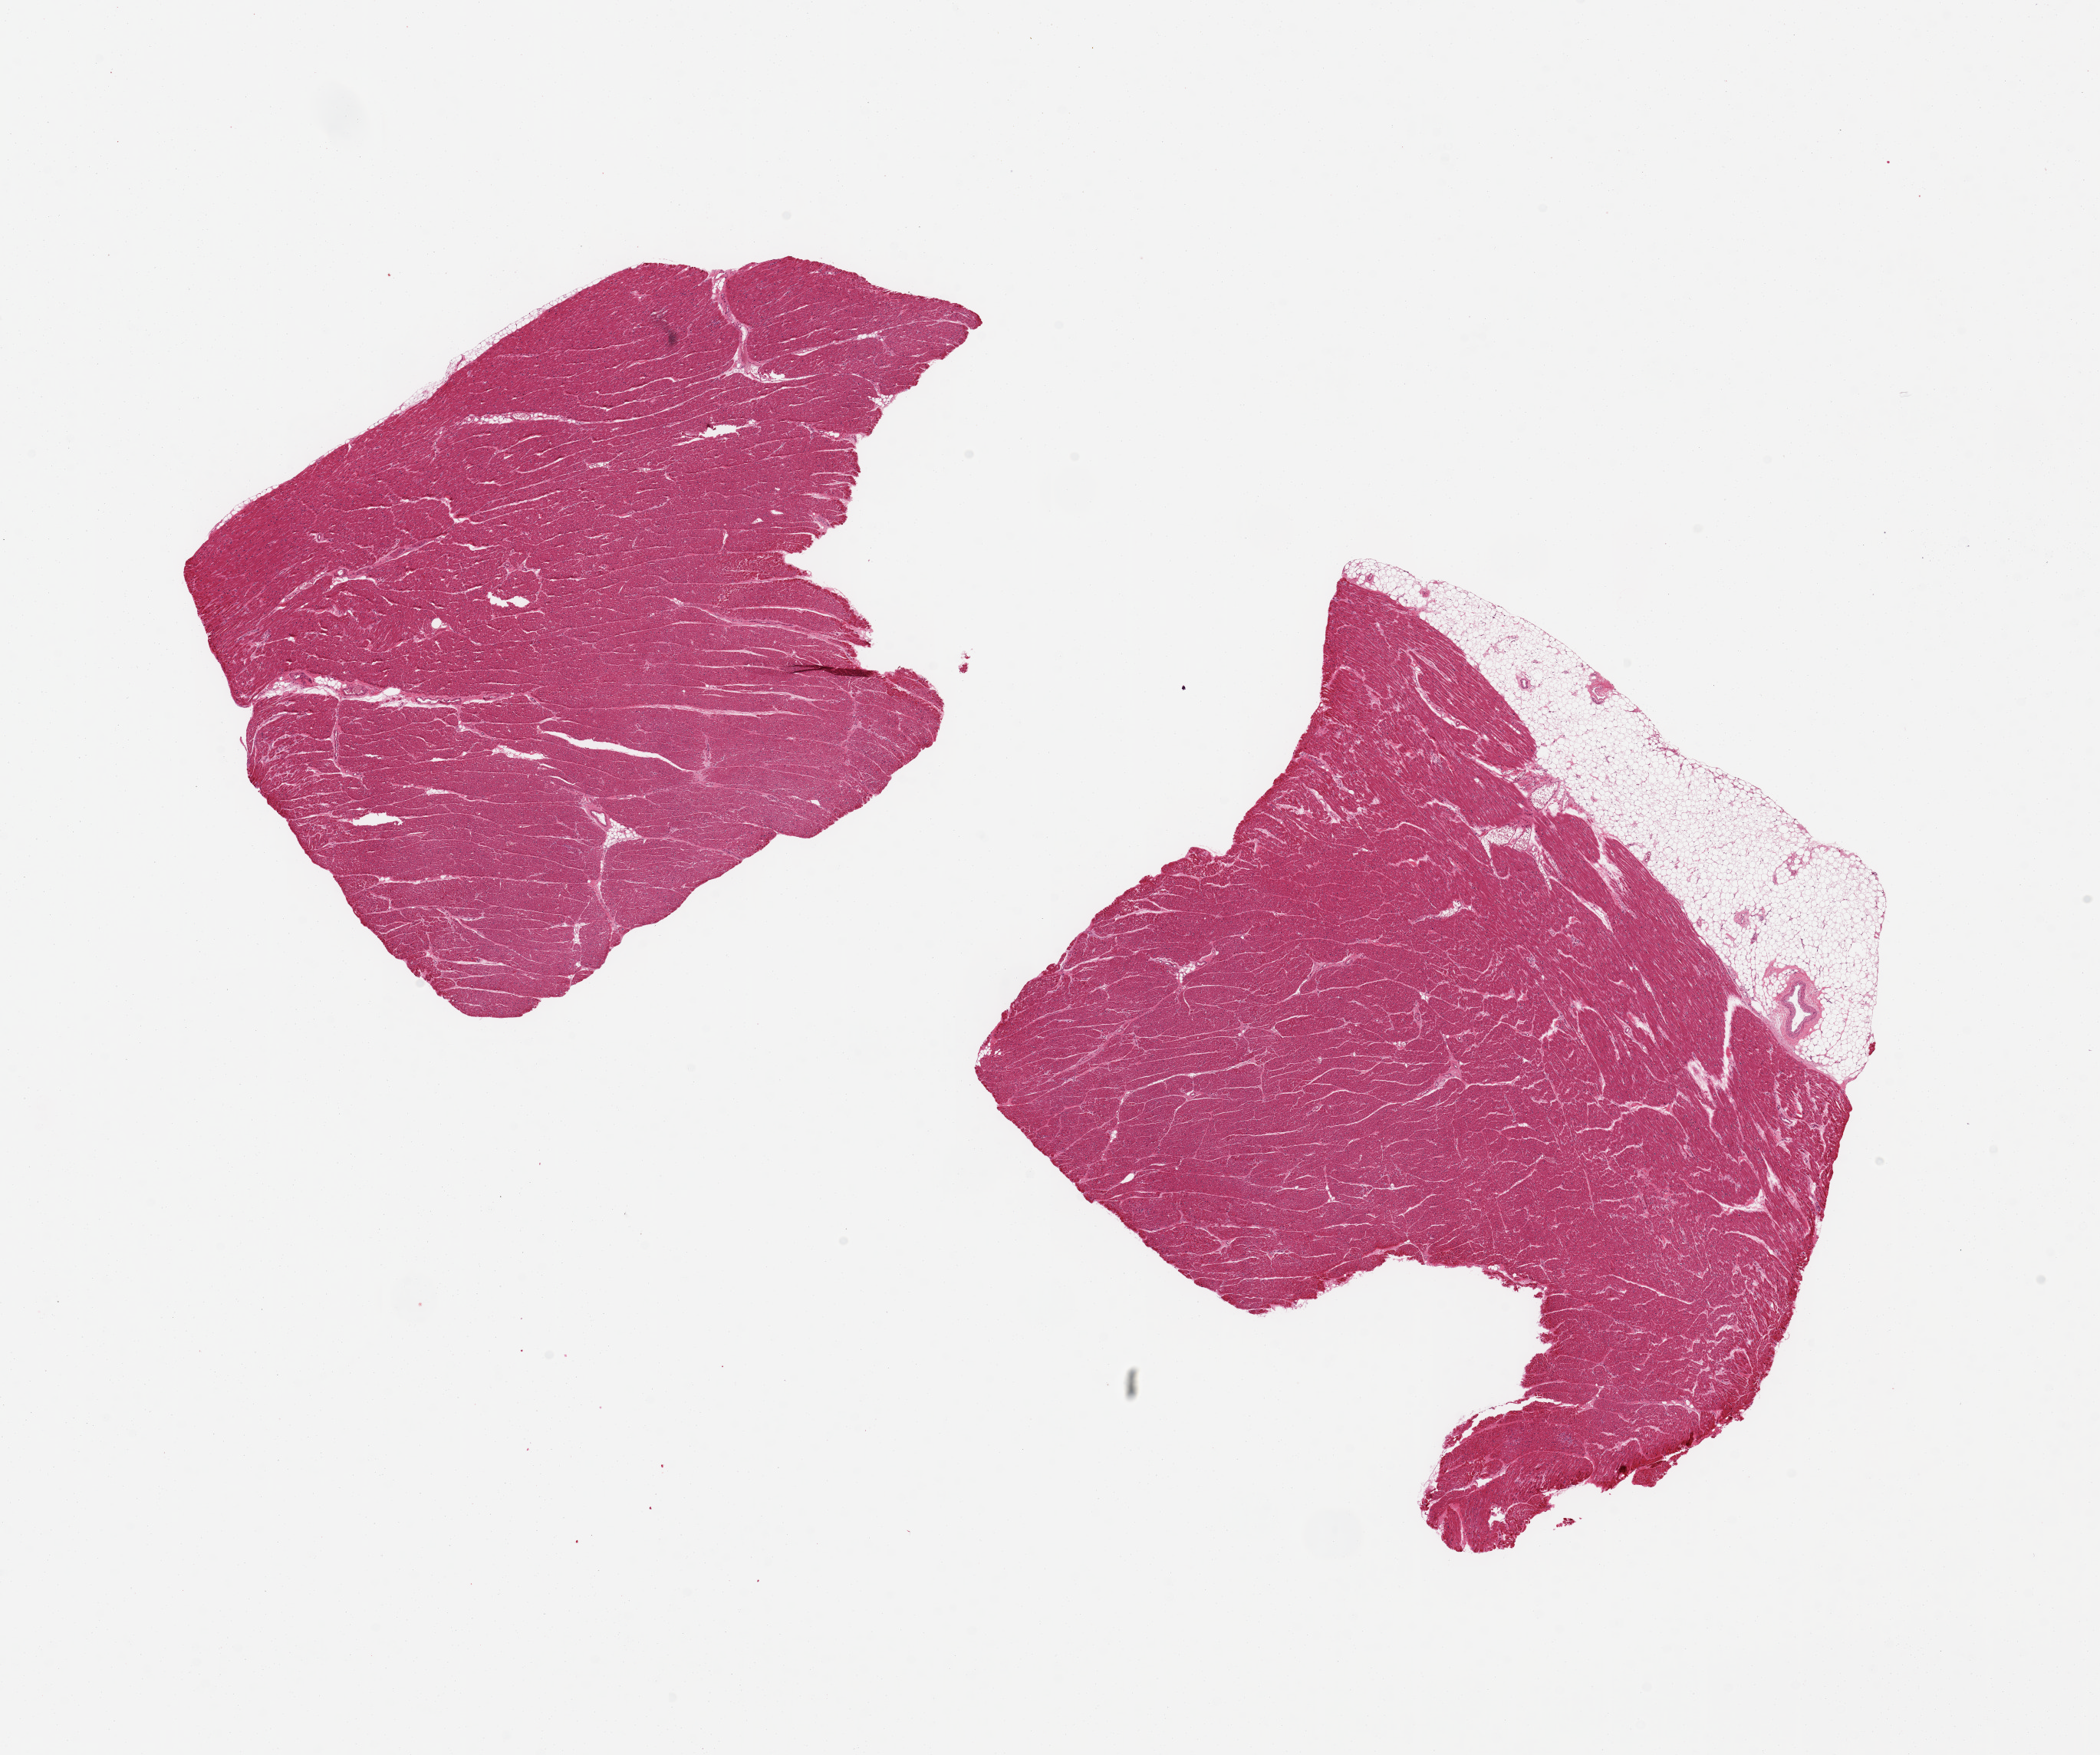
Whole-slide image, hematoxylin and eosin (H&E) stain, brightfield — whole scanned area (about 21.7 x 18.1 mm, from a 20x scan) shown as a low-resolution overview, PAXgene-fixed paraffin-embedded (PFPE) section, target tissue: heart, tissue donor sample. Female donor.
• pathologist's review note for this sample: 2 aliquots, ~8x6mm. Mild ischemic changes